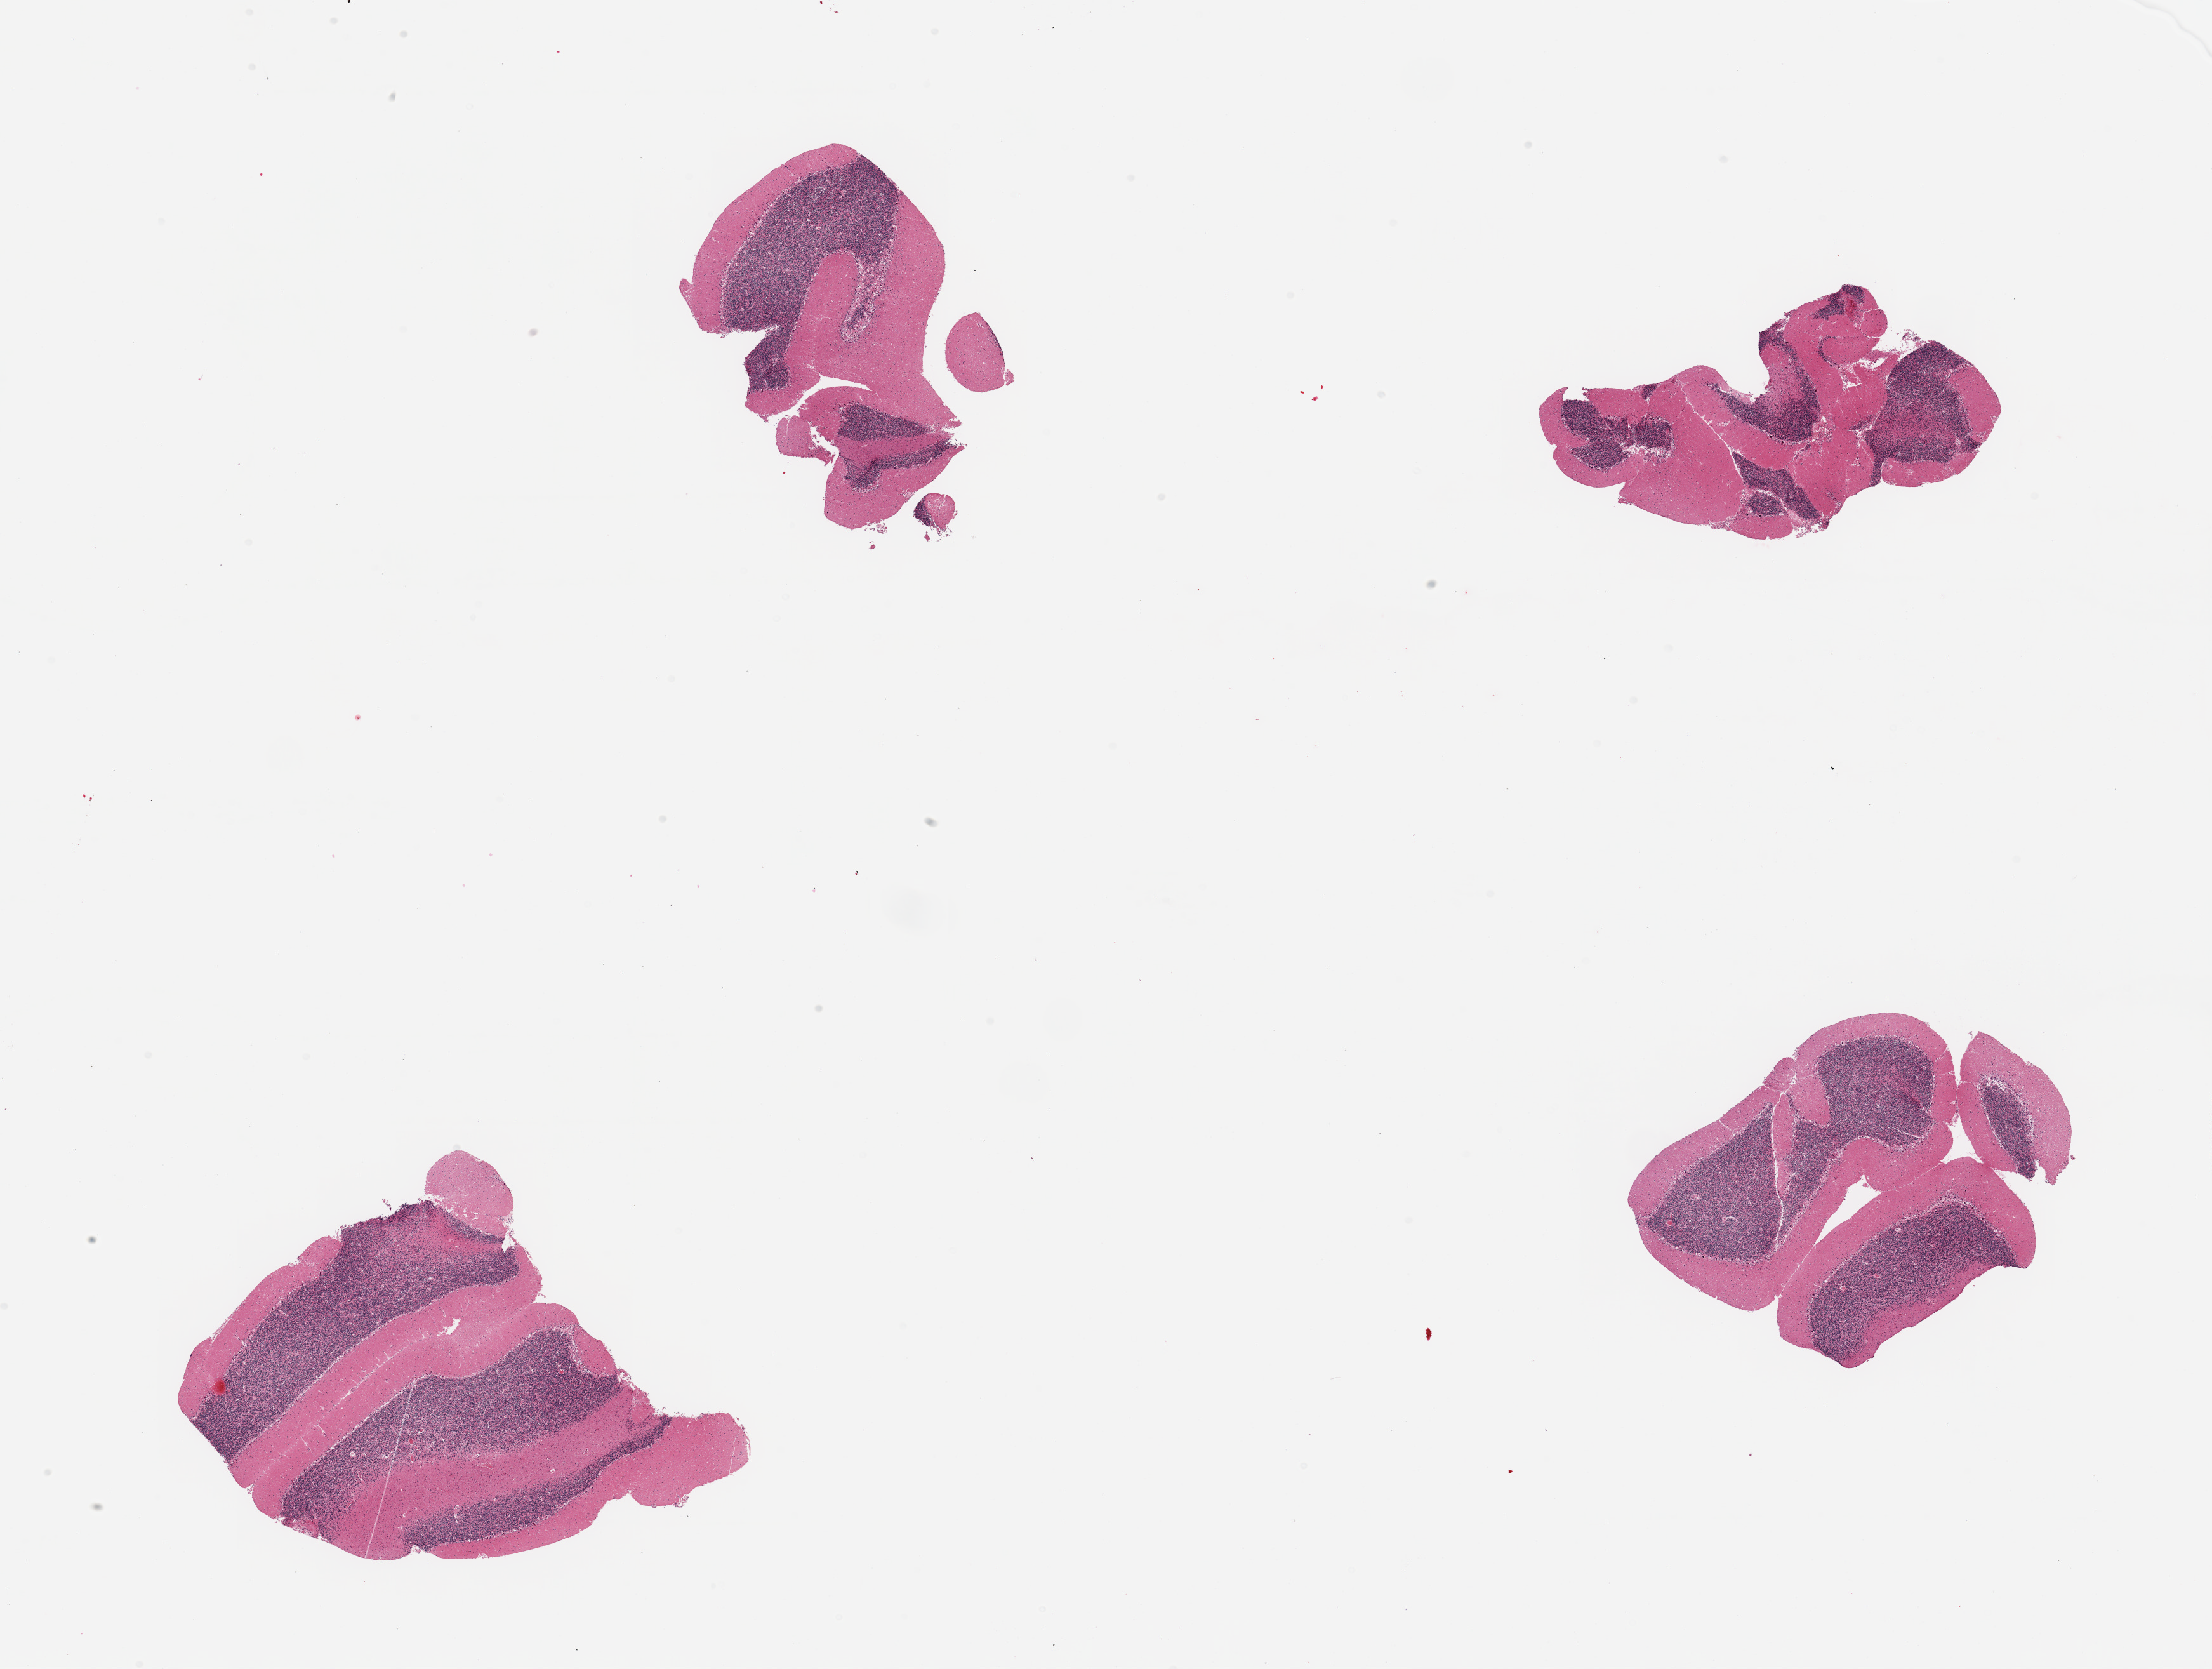
Hematoxylin and eosin (H&E) whole-slide image, a low-resolution overview of the entire scanned area, about 27.6 x 20.8 mm; PAXgene-fixed, paraffin-embedded tissue; target tissue: cerebellum; donor tissue sample. Donor sex: female.
- reviewer comment on this tissue sample: 4 pieces